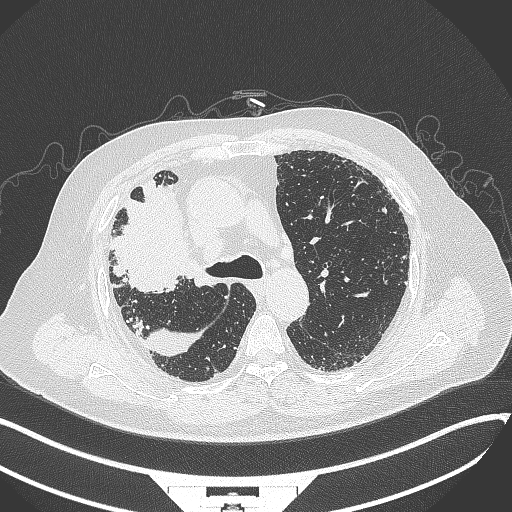
Chest CT, one axial slice; slice 236 of 384 in the series (ordered by position); reconstruction kernel B70f; lung window (W 1500 / L -600 HU); 1 mm slice thickness; 512 × 512 image matrix. Male patient, age 69 years. From the clinical record (not read from this slice): clinical TNM (as recorded): T4 N3 M1.
Structures marked on this image (bounding box drawn by a radiologist):
- lung tumour (recorded histology: adenocarcinoma): bounding box [x1, y1, x2, y2] px = [107, 173, 194, 296]